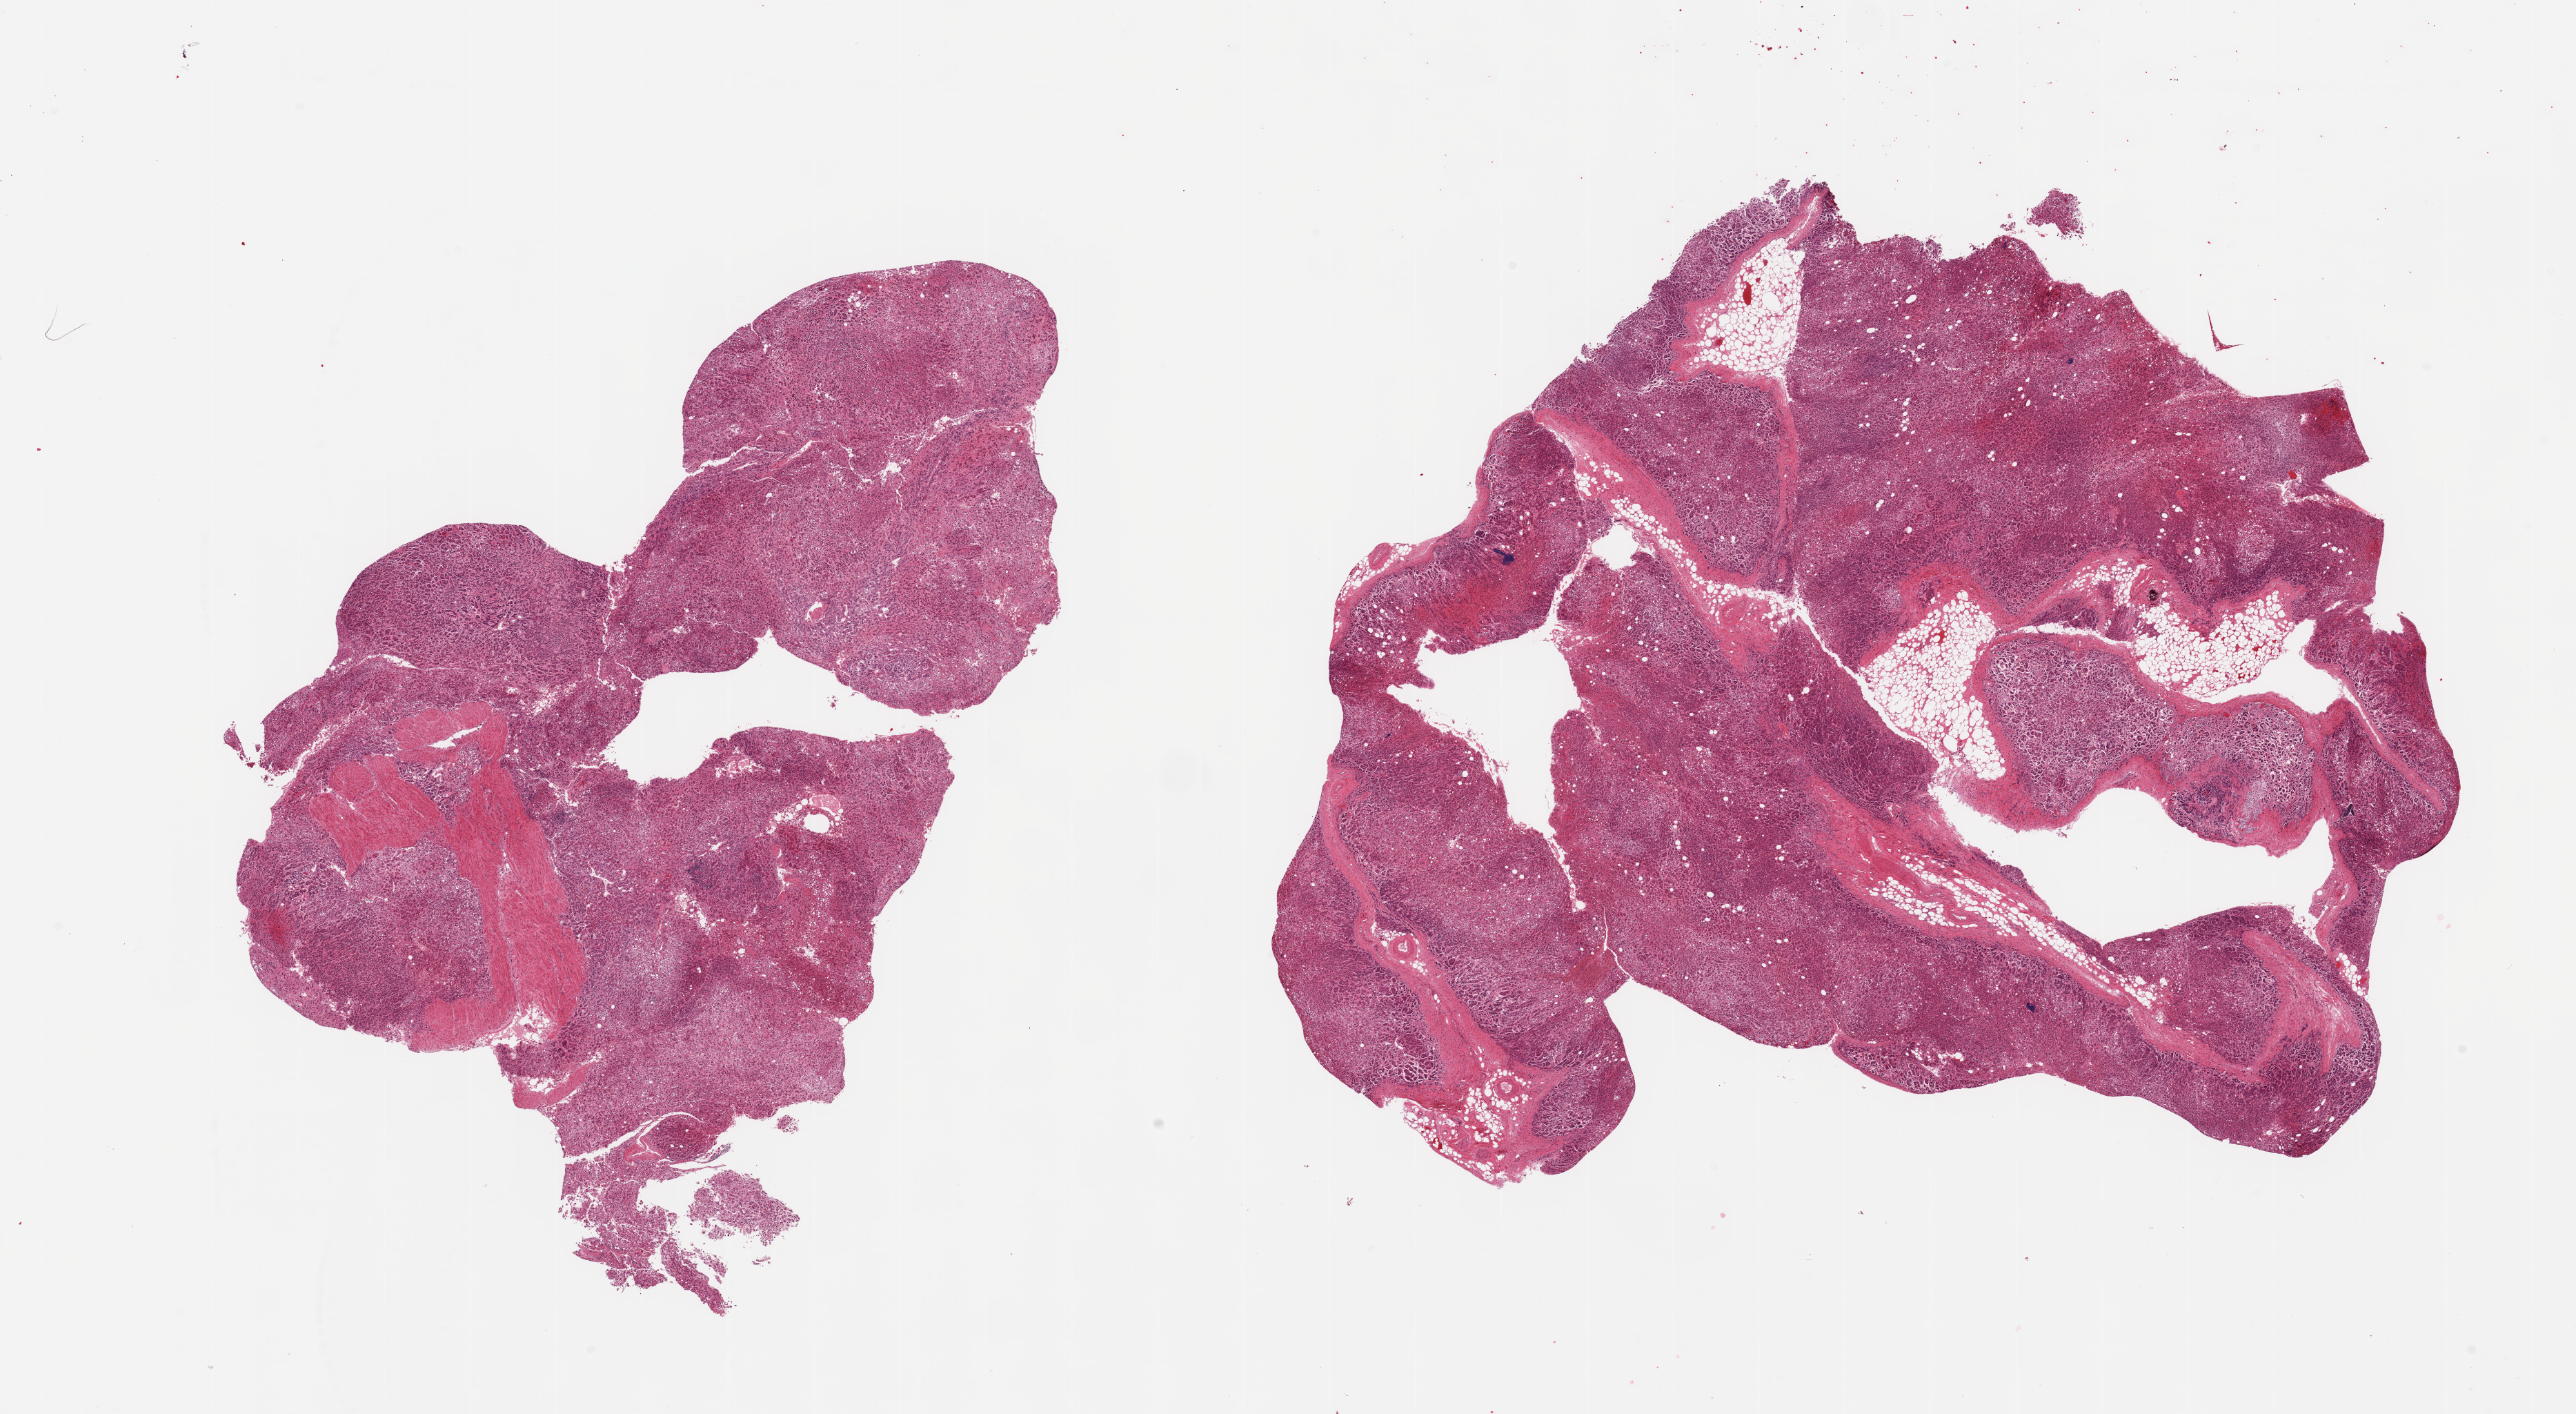
Digitized H&E-stained section — whole scanned area (about 29.5 x 16.2 mm) shown as a low-resolution overview, PAXgene-fixed paraffin-embedded (PFPE) section, section of adrenal gland (target tissue), tissue donor sample. Male donor.
* review note (as recorded): 2 pieces; oversized